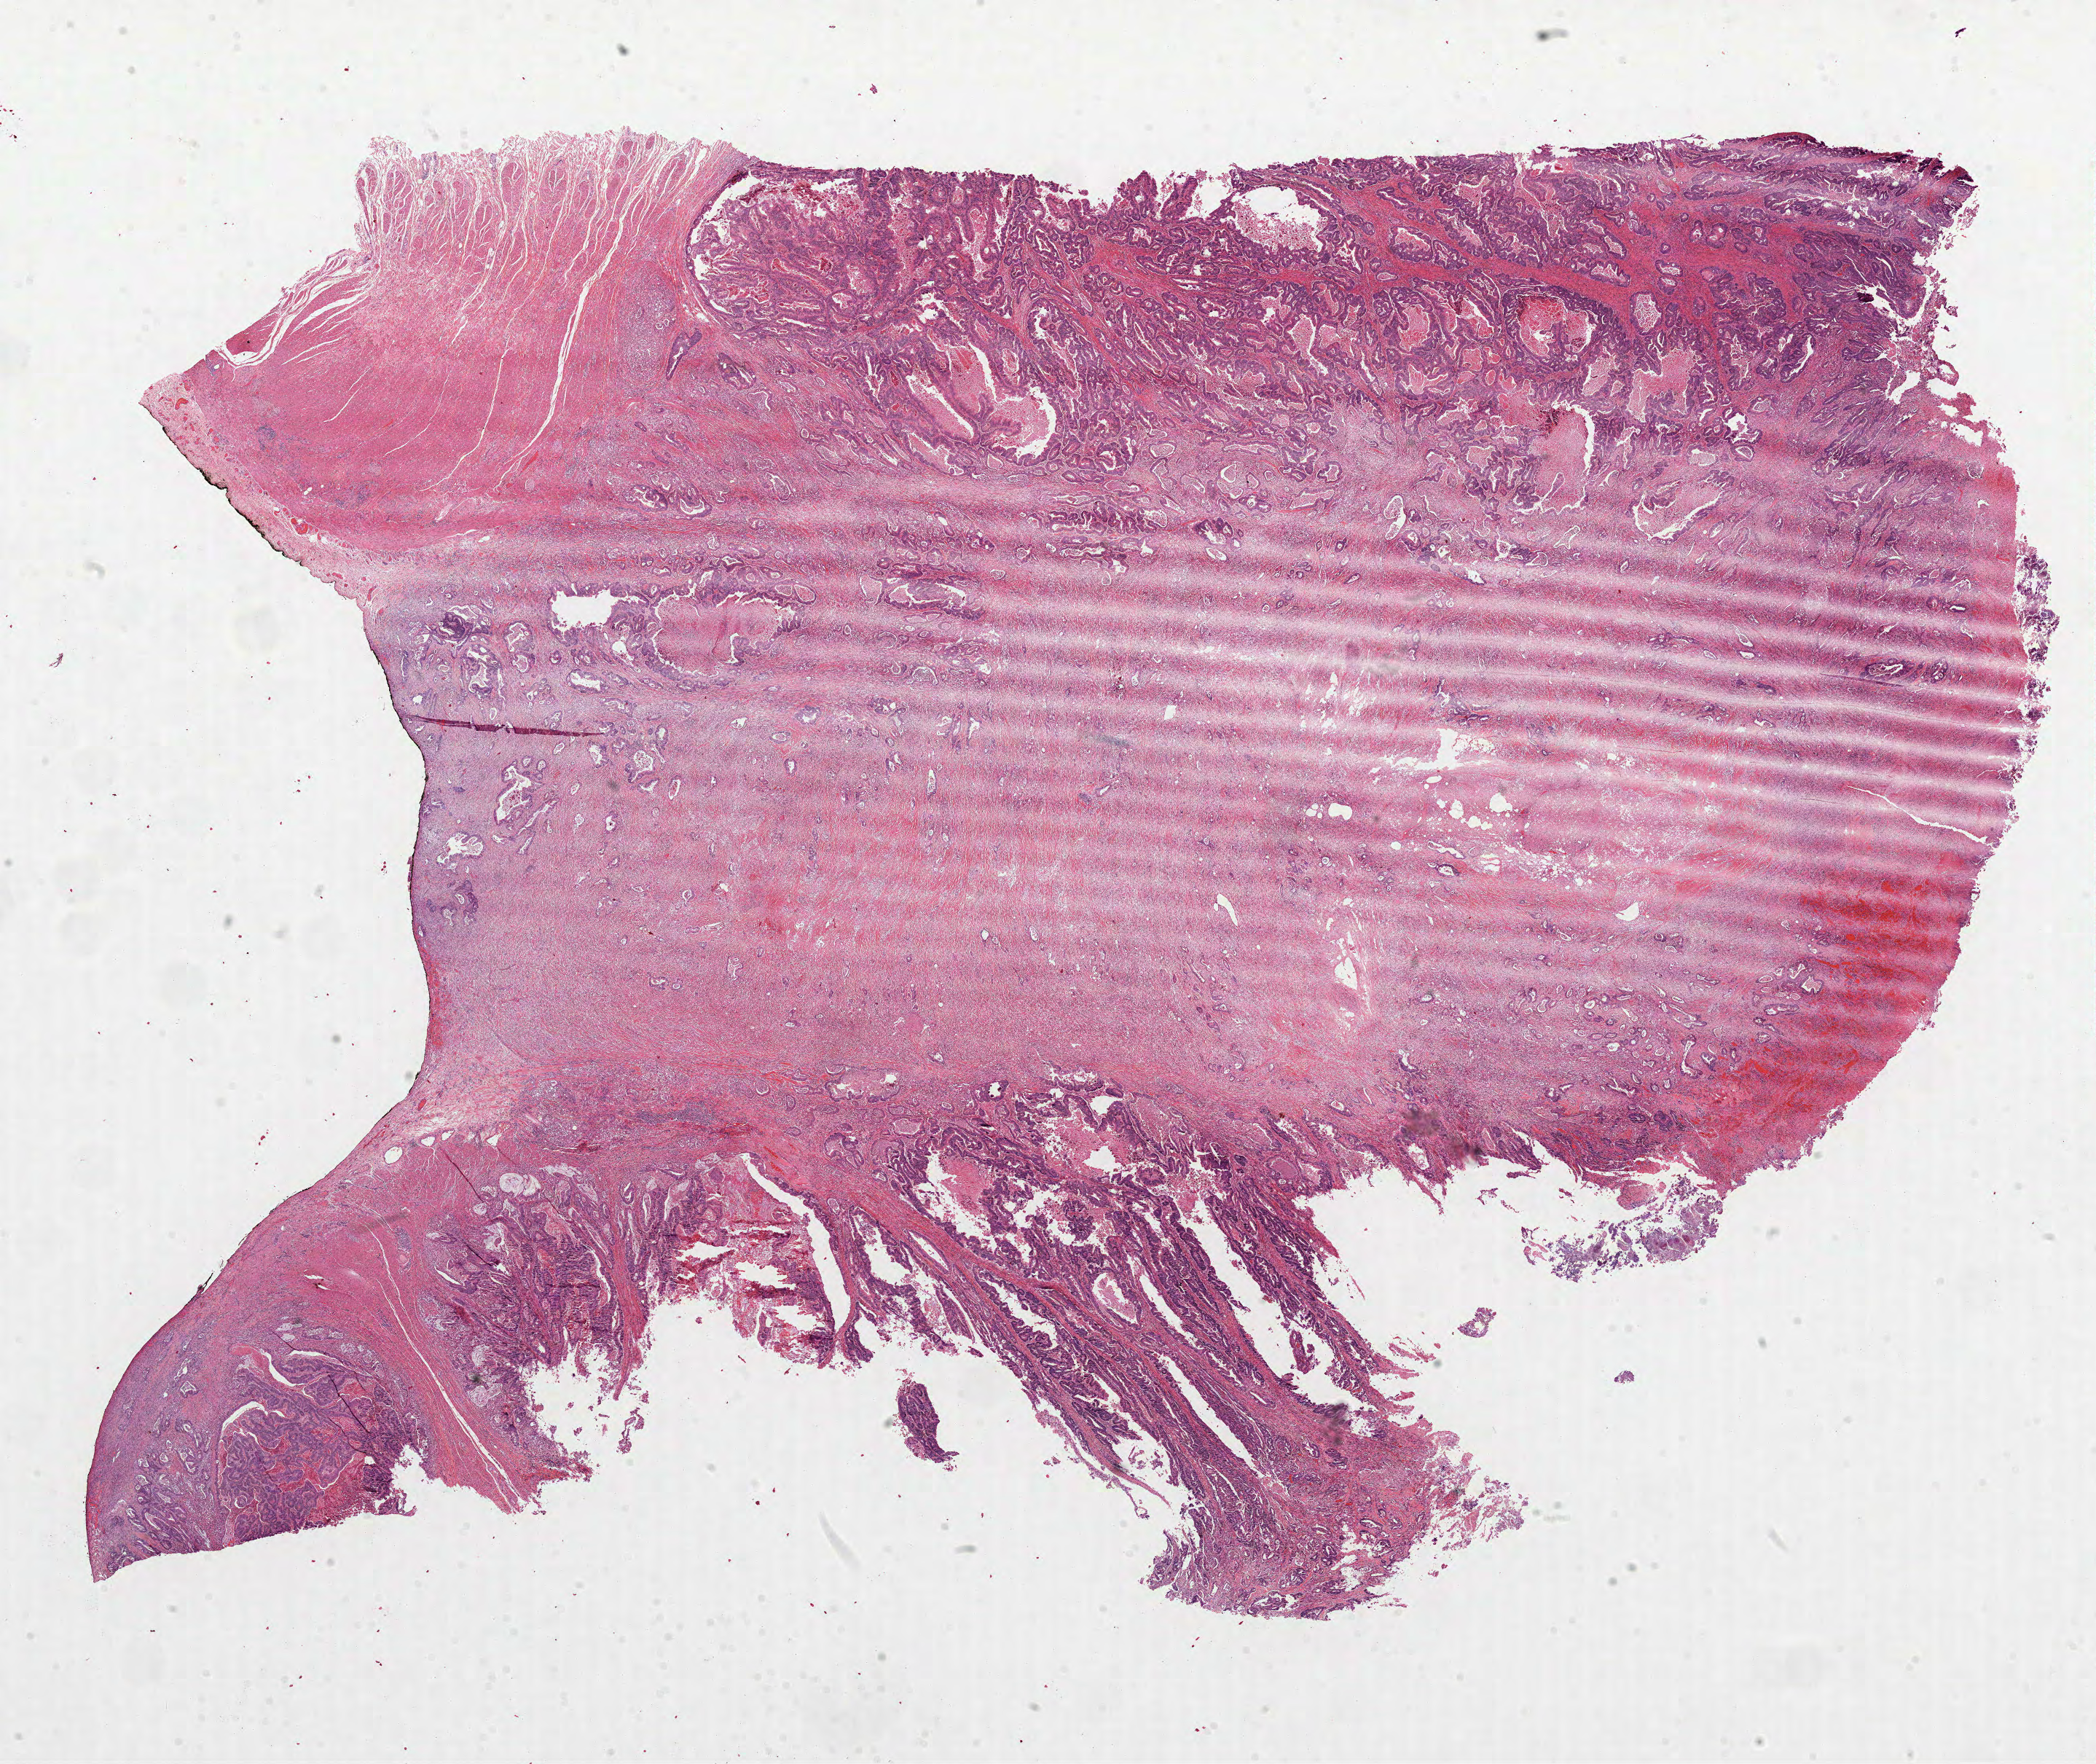
Hematoxylin and eosin (H&E) stained whole-slide image — a low-resolution overview of the entire scanned area, about 23.2 x 19.5 mm (from a 40x scan). FFPE section. Colon, primary tumour sample. Patient: male, age at initial diagnosis 81 years.
AJCC pathologic stage: IV (6th edition). Pathologic diagnosis: Adenocarcinoma, NOS (cecum). Lymph nodes positive (case pathology): 10 of 17 examined.